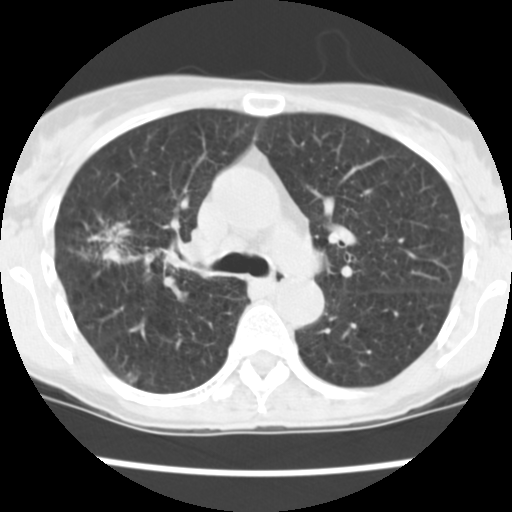
Low-dose screening chest CT, one axial slice. Position 160 of 252 along the scan axis. 120 kVp. Lung window (W 1500 / L -600 HU). 512 × 512 image matrix.
Structures marked on this image (outlined manually by an expert reader):
- lesion 1 (tumor, upper lobe of right lung): bounding box (x1, y1, x2, y2) in pixels: (125, 371, 138, 386)
- lesion 2 (tumor, lower lobe of right lung): (101, 223, 131, 263)